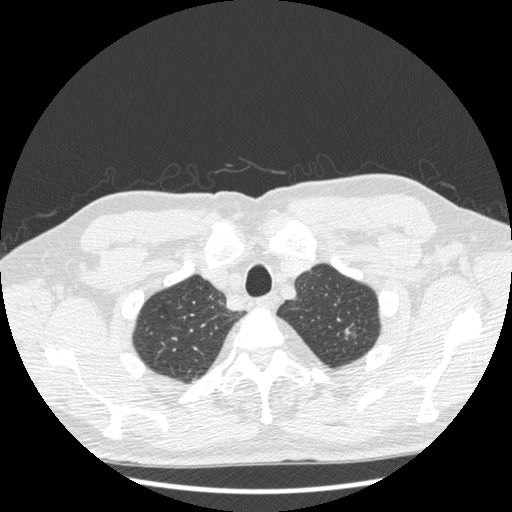
Low-dose screening chest CT, one axial slice; position 191 of 223 along the scan axis; reconstruction kernel STANDARD; 120 kVp; lung window (W 1500 / L -600 HU); 1.25 mm slice thickness; 512 × 512 image matrix, field of view 380 × 380 mm.
Structures marked on this image (expert manual segmentation):
- lesion 1 (tumor, upper lobe of left lung): box from (x=345, y=327) to (x=351, y=339) px